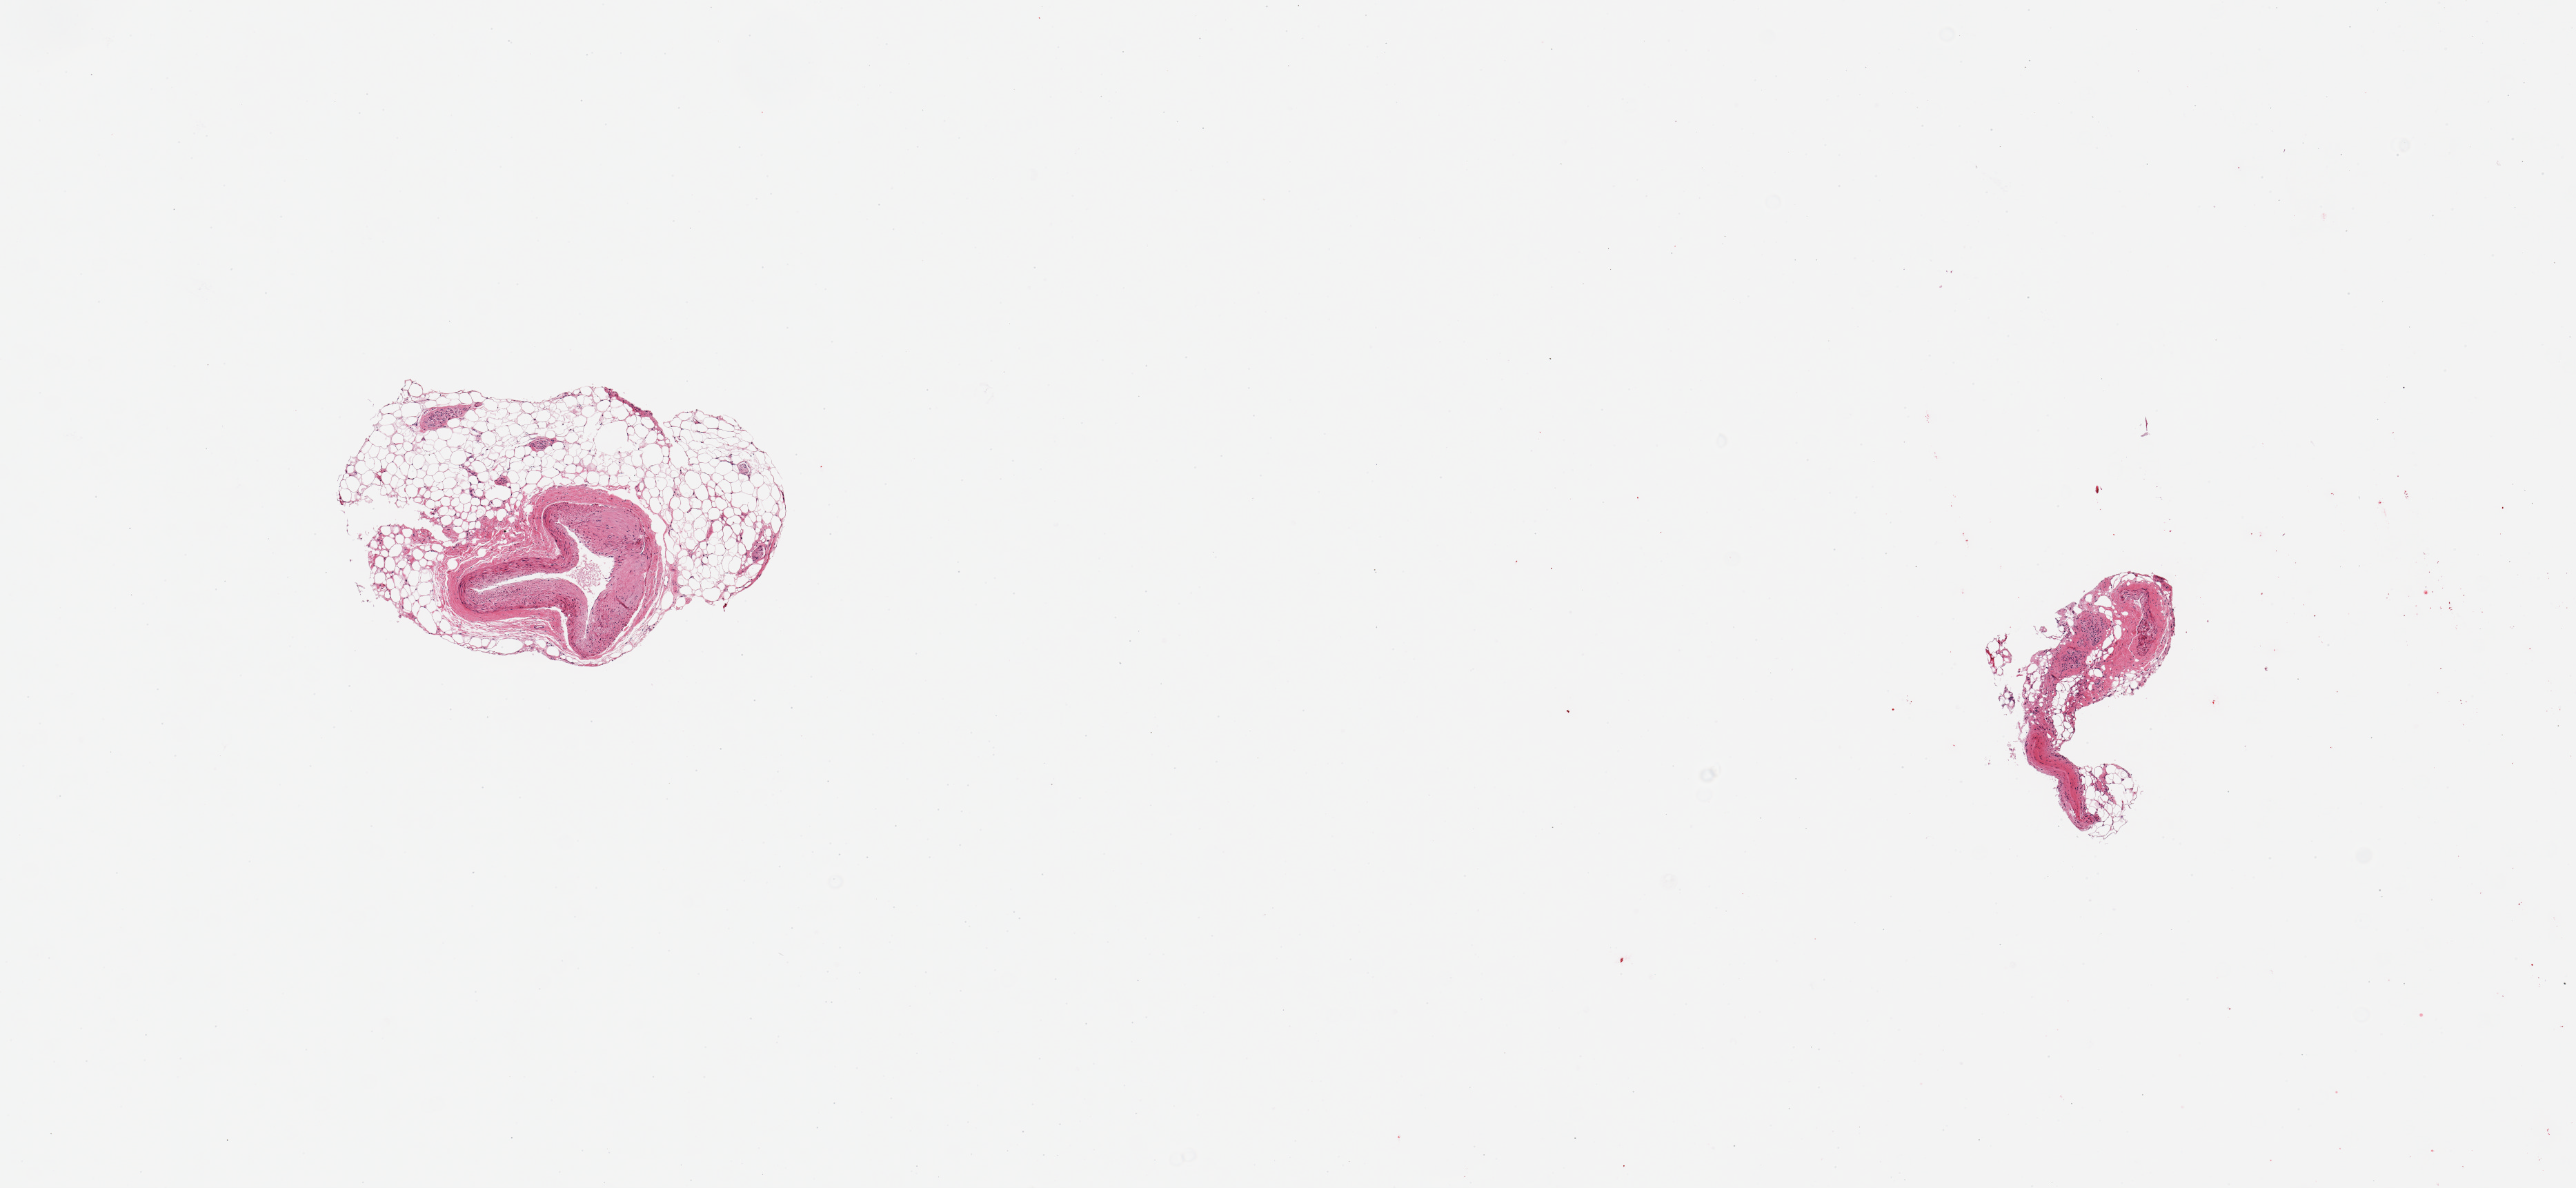
Digitized haematoxylin and eosin-stained section, a low-resolution overview of the entire scanned area, about 14.8 x 6.8 mm; PAXgene-fixed, paraffin-embedded tissue; section of coronary artery (target tissue); tissue donor sample. Male donor.
• pathologist's review note for this sample: 2 pieces; small vessels with 30 & 60% external fat